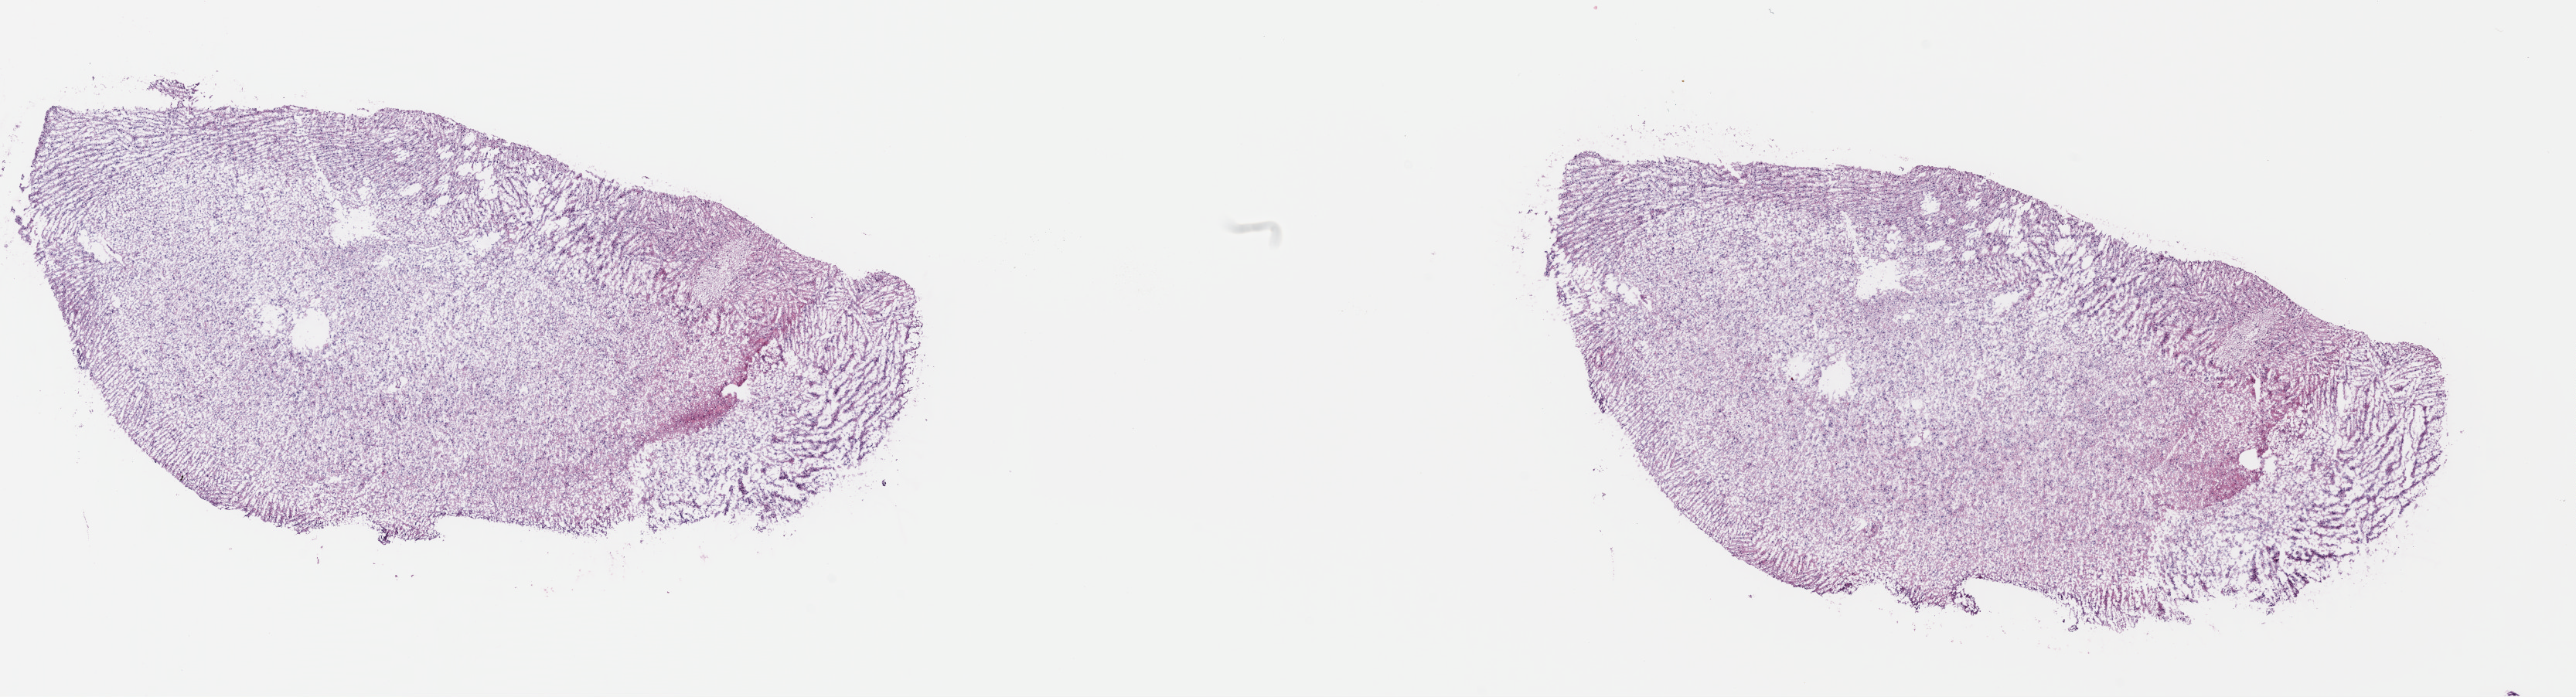
Whole-slide histology image, H&E-stained, low-resolution overview of the scanned area, about 26.2 x 7.1 mm (from a 40x scan); frozen section from the top of the tissue portion; brain, primary tumour sample. Patient: female, age at initial diagnosis 27 years. Histologic grade: G3 (poorly differentiated). Slide review estimates, as recorded: tumour cells 40%, tumour nuclei 80%, normal cells 10%, stromal cells 50%, necrosis 0%. Infiltration values recorded for this section: lymphocyte infiltration 0%, monocyte infiltration 0%, neutrophil infiltration 0%.
- laterality: left
- histologic diagnosis: Astrocytoma, anaplastic (cerebrum)